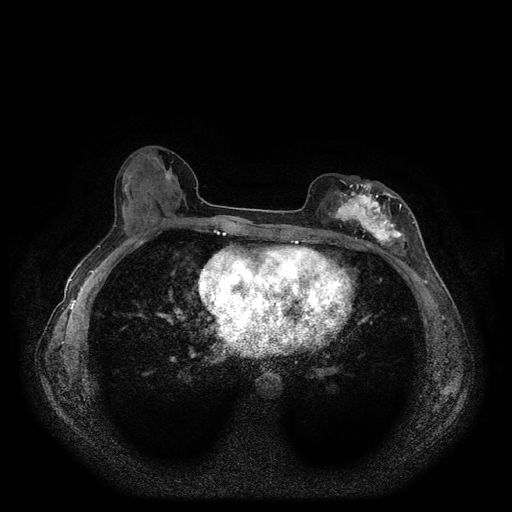
Breast MRI (dynamic contrast-enhanced, multi-phase), one axial slice. Position 50 of 116 along the scan axis. Dynamic contrast-enhanced series, time point 2 of 5 at this slice position (early post-contrast). 1.5 T. TE 2.6 ms, TR 5.3 ms. 512 × 512 image matrix, field of view 350 × 350 mm. Patient: female, 51 years.
Structures marked on this image (semi-automatically segmented with operator editing):
- breast lesion (labelled 'tumour' in the annotation; benign lesions carry a separate 'benign' label): bounding box <325,179,408,251> (left, top, right, bottom; pixels)
- breast lesion (labelled benign in the annotation): <161,167,176,183>